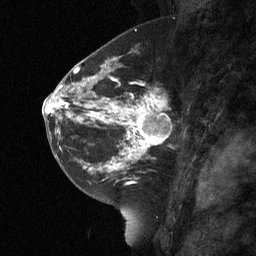
Breast MRI (dynamic contrast-enhanced), one sagittal slice. Slice 34 of 64 in the series (ordered by position). Dynamic contrast-enhanced study with each time point stored as its own series, time point 2 of 3 at this slice position (early post-contrast, ordered by acquisition time). 1.5 T. TE 4.8 ms, TR 27 ms. 2 mm slice thickness. 256 × 256 image matrix, field of view 180 × 180 mm. Patient: female, 42 years. Case-level facts recorded for this patient, not image findings: setting: breast cancer imaged before/during neoadjuvant chemotherapy; receptor status: triple-negative.
Annotated regions visible in this slice (semi-automatic segmentation, software-assisted and operator-edited):
- analysis volume of interest (the breast-tissue region the enhancement analysis was run in; not a lesion): bounding box [x1, y1, x2, y2] px = [115, 85, 186, 160]
- tumour enhancement mask (voxels above the 90 % enhancement threshold inside the analysis volume of interest): [115, 91, 169, 160]